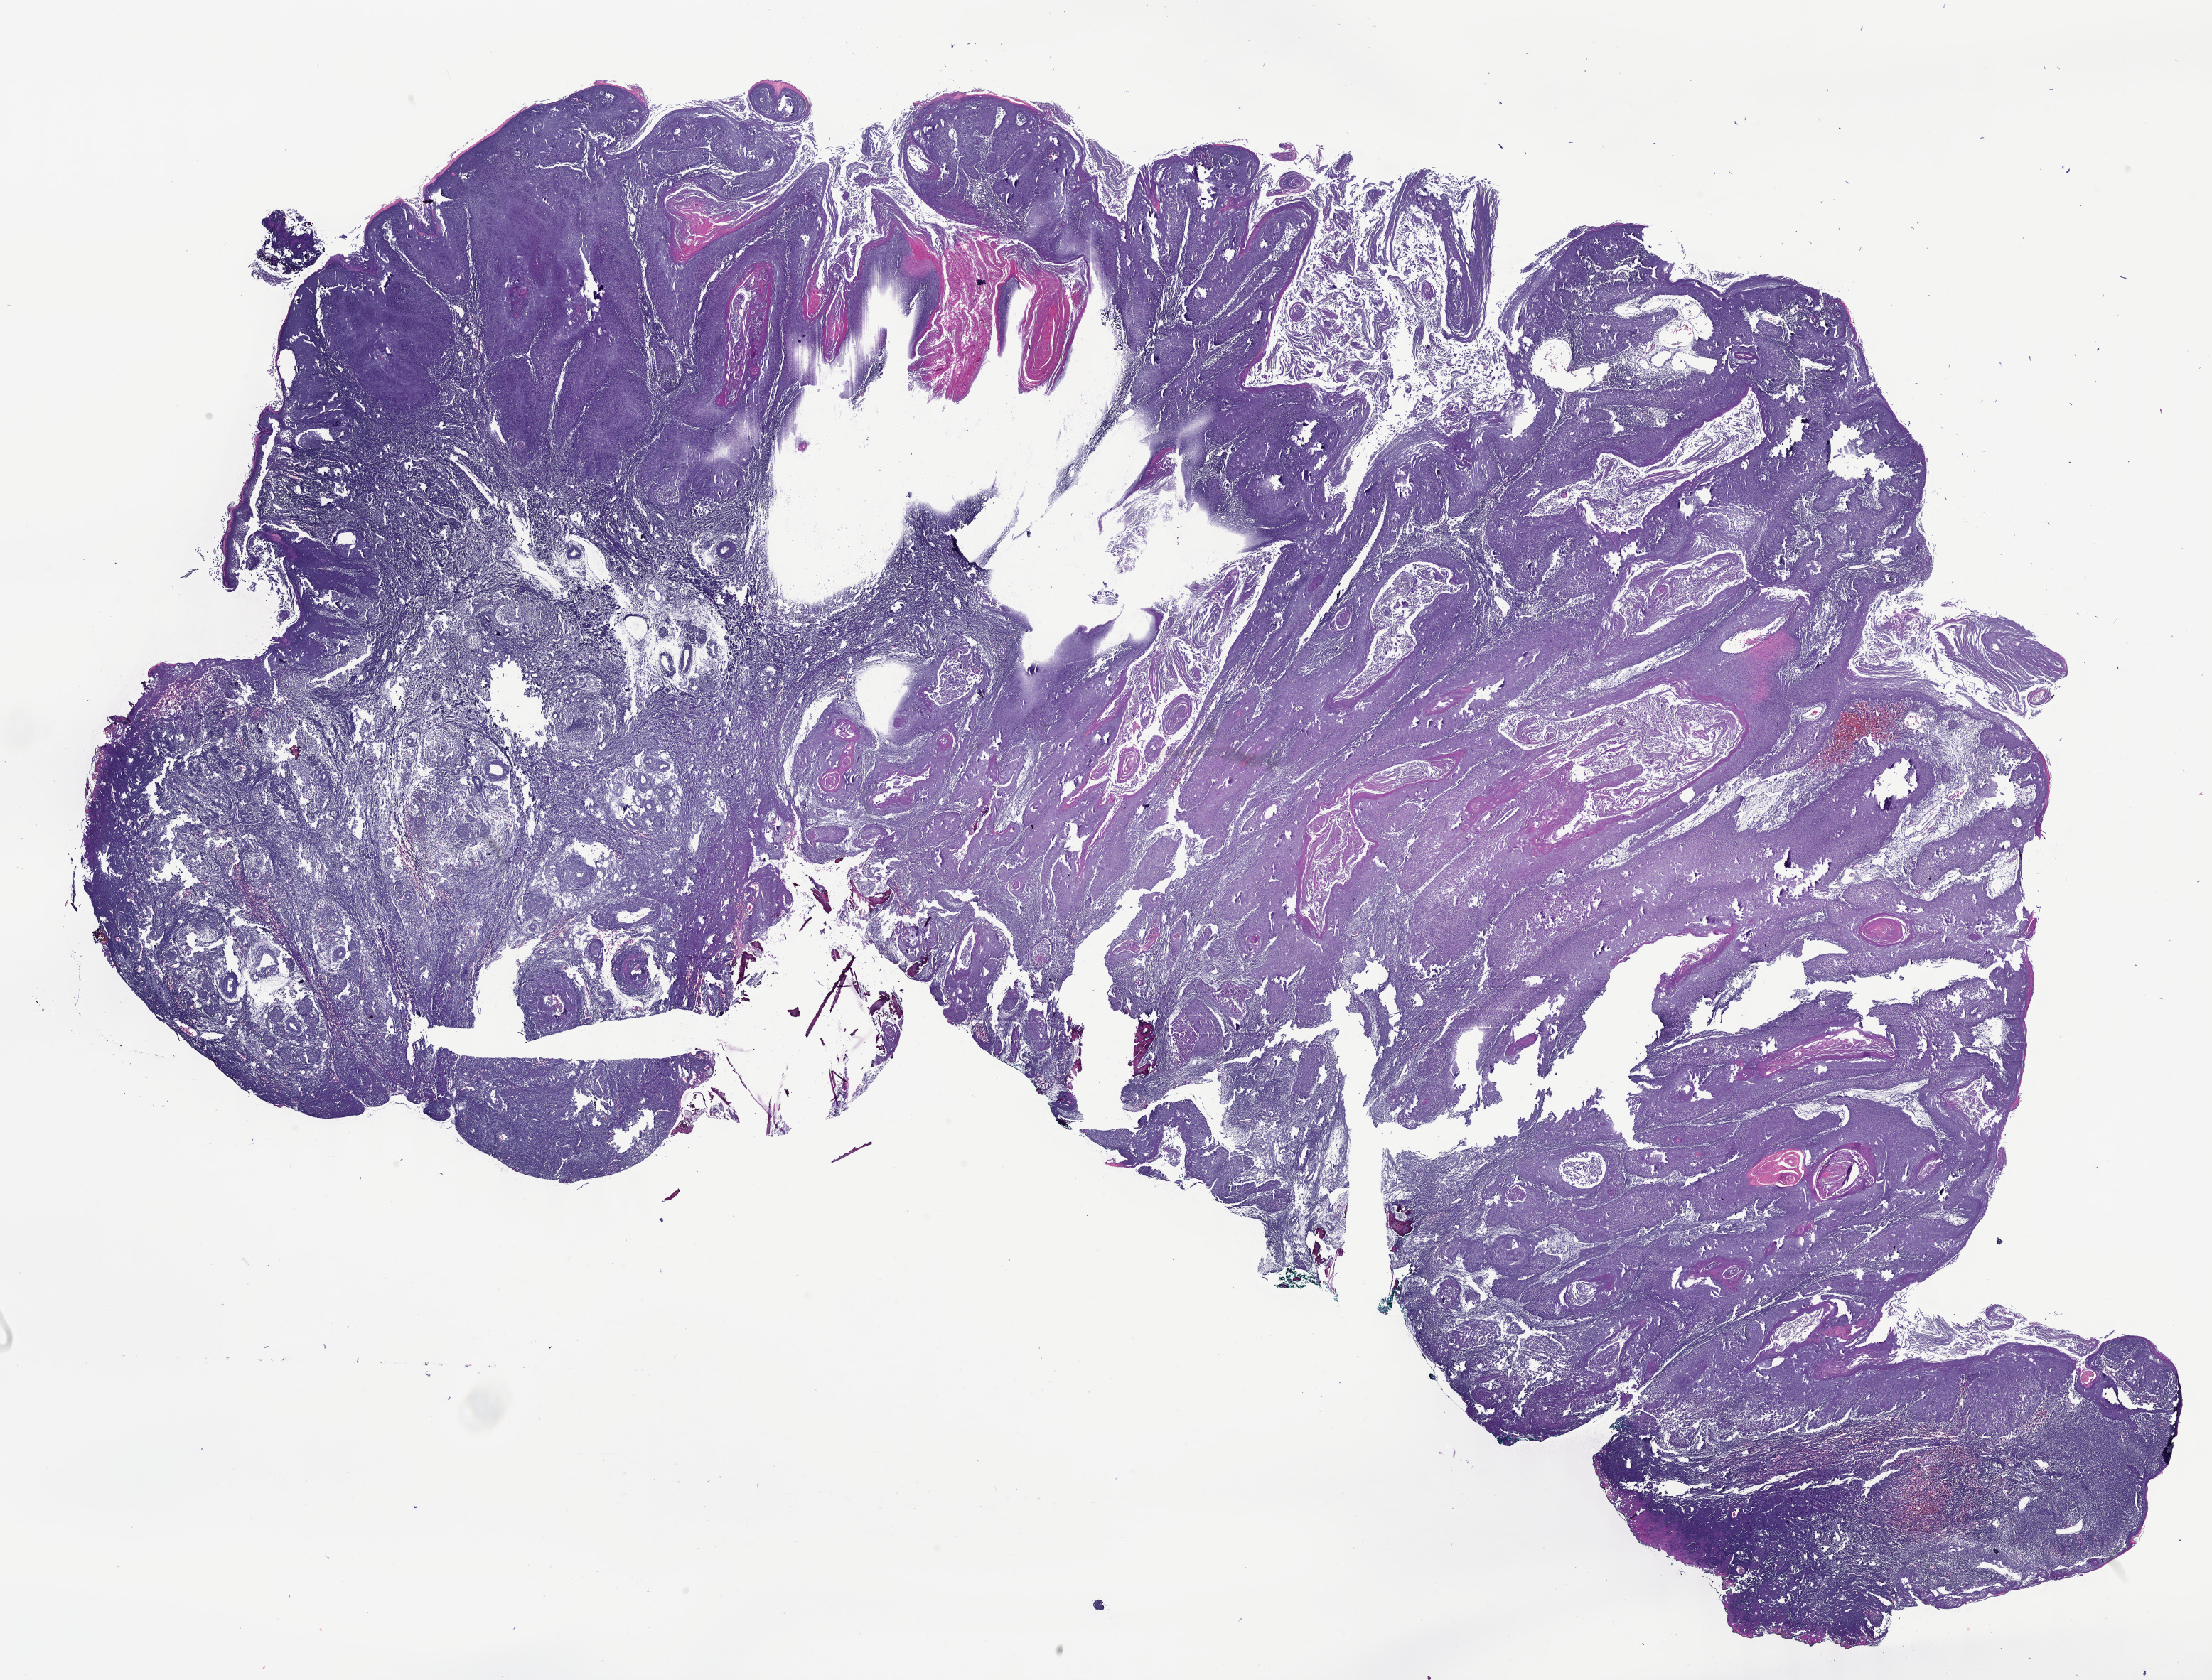
Digitized H&E tissue section (whole slide), shown as a low-resolution overview of the whole scanned area (about 25.1 x 19.1 mm, slide scanned at 40x). FFPE section. Sample: primary tumour, head and neck. Patient: female, age at initial diagnosis 77 years. Histologic grade: G1 (well differentiated).
• laterality: right
• diagnosis: Squamous cell carcinoma, NOS (overlapping lesion of lip, oral cavity and pharynx)
• AJCC pathologic stage: III (7th edition)